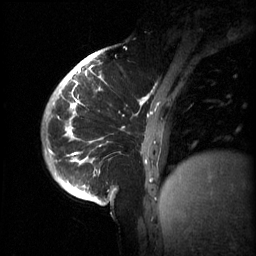
Breast MRI (dynamic contrast-enhanced), one sagittal slice; position 13 of 60 along the scan axis; 3 images stored at this slice position (order not interpretable as contrast timing); 1.5 T; TE 4.2 ms, TR 11 ms; 256 × 256 image matrix, field of view 220 × 220 mm. Female patient, age 51 years.
Annotated regions visible in this slice (semi-automatically segmented with operator editing):
- analysis volume of interest (the breast-tissue region the enhancement analysis was run in; not a lesion): bounding box (x1, y1, x2, y2) in pixels: (63, 80, 187, 201)
- tumour enhancement mask (voxels above the 70 % enhancement threshold inside the analysis volume of interest): (66, 80, 168, 187)